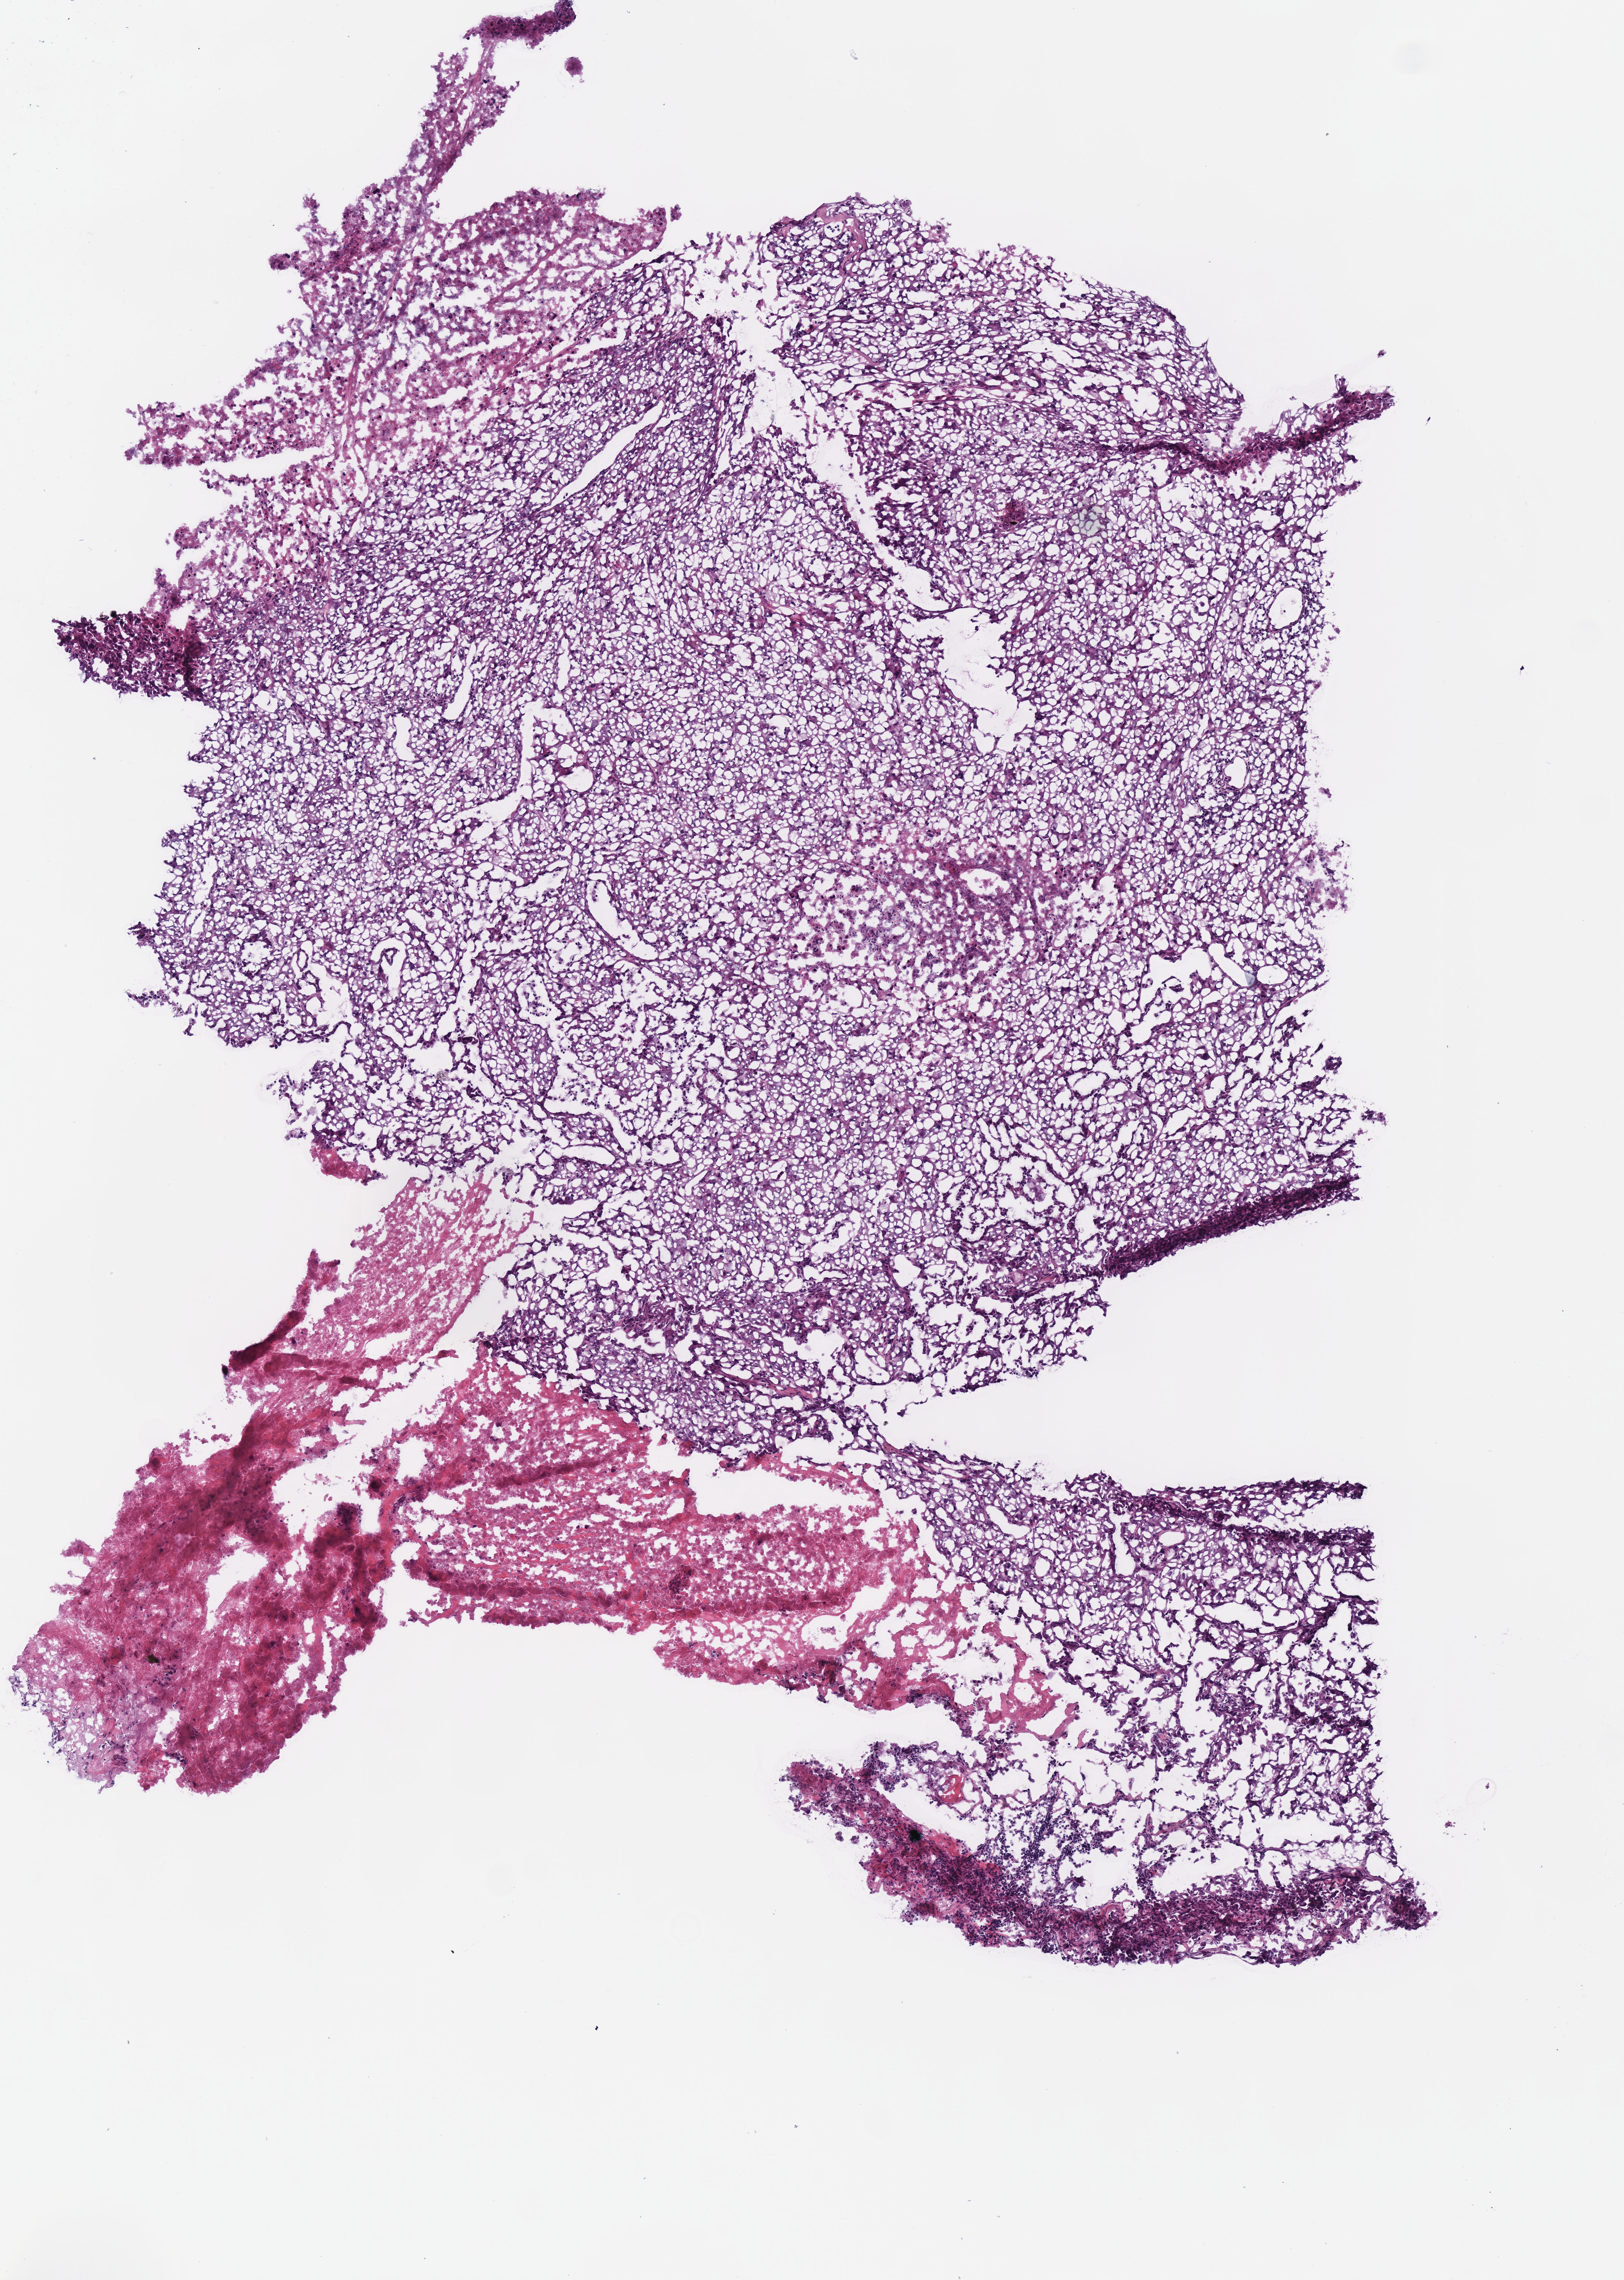
Whole-slide histology image, Hematoxylin and eosin (H&E) stained — low-resolution overview of the scanned area, about 4.2 x 5.9 mm (slide scanned at 40x), frozen section, sample: primary tumour, lung. Male patient; age at initial diagnosis 56 years. Pathologist review of this section (percent, as recorded): tumour cells 81%, tumour nuclei 80%, normal cells 0%, stromal cells 0%, necrosis 19%. Inflammatory infiltration, as recorded: lymphocyte infiltration 5%, monocyte infiltration 2%, neutrophil infiltration 0%.
- diagnosis: Adenocarcinoma, NOS
- AJCC pathologic stage: IB (6th edition)